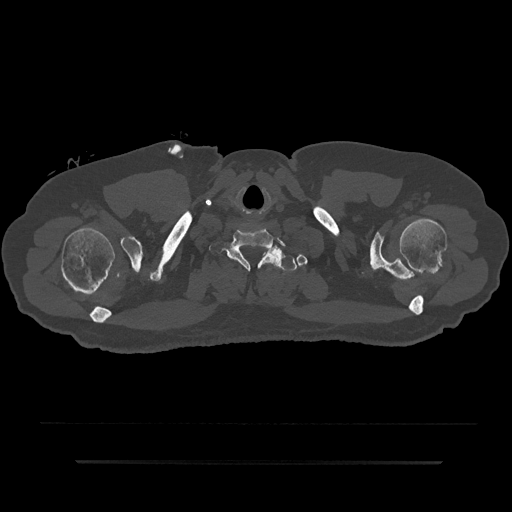
CT including the spine, one axial slice. Slice 764 of 797 in the series (ordered by position). Reconstruction kernel Br40s/3. 120 kVp. Bone window (W 1800 / L 400 HU). 0.5 mm slice thickness. 512 × 512 image matrix, field of view 464 × 464 mm. Patient: male, 59 years. From the clinical record (not read from this slice): primary cancer: bile ducts; vertebrae with lytic lesions (as recorded): T10.
Outlined on this slice (semi-automatically segmented with operator editing):
- T1 vertebra: bounding box (x1, y1, x2, y2) in pixels: (243, 250, 302, 271)